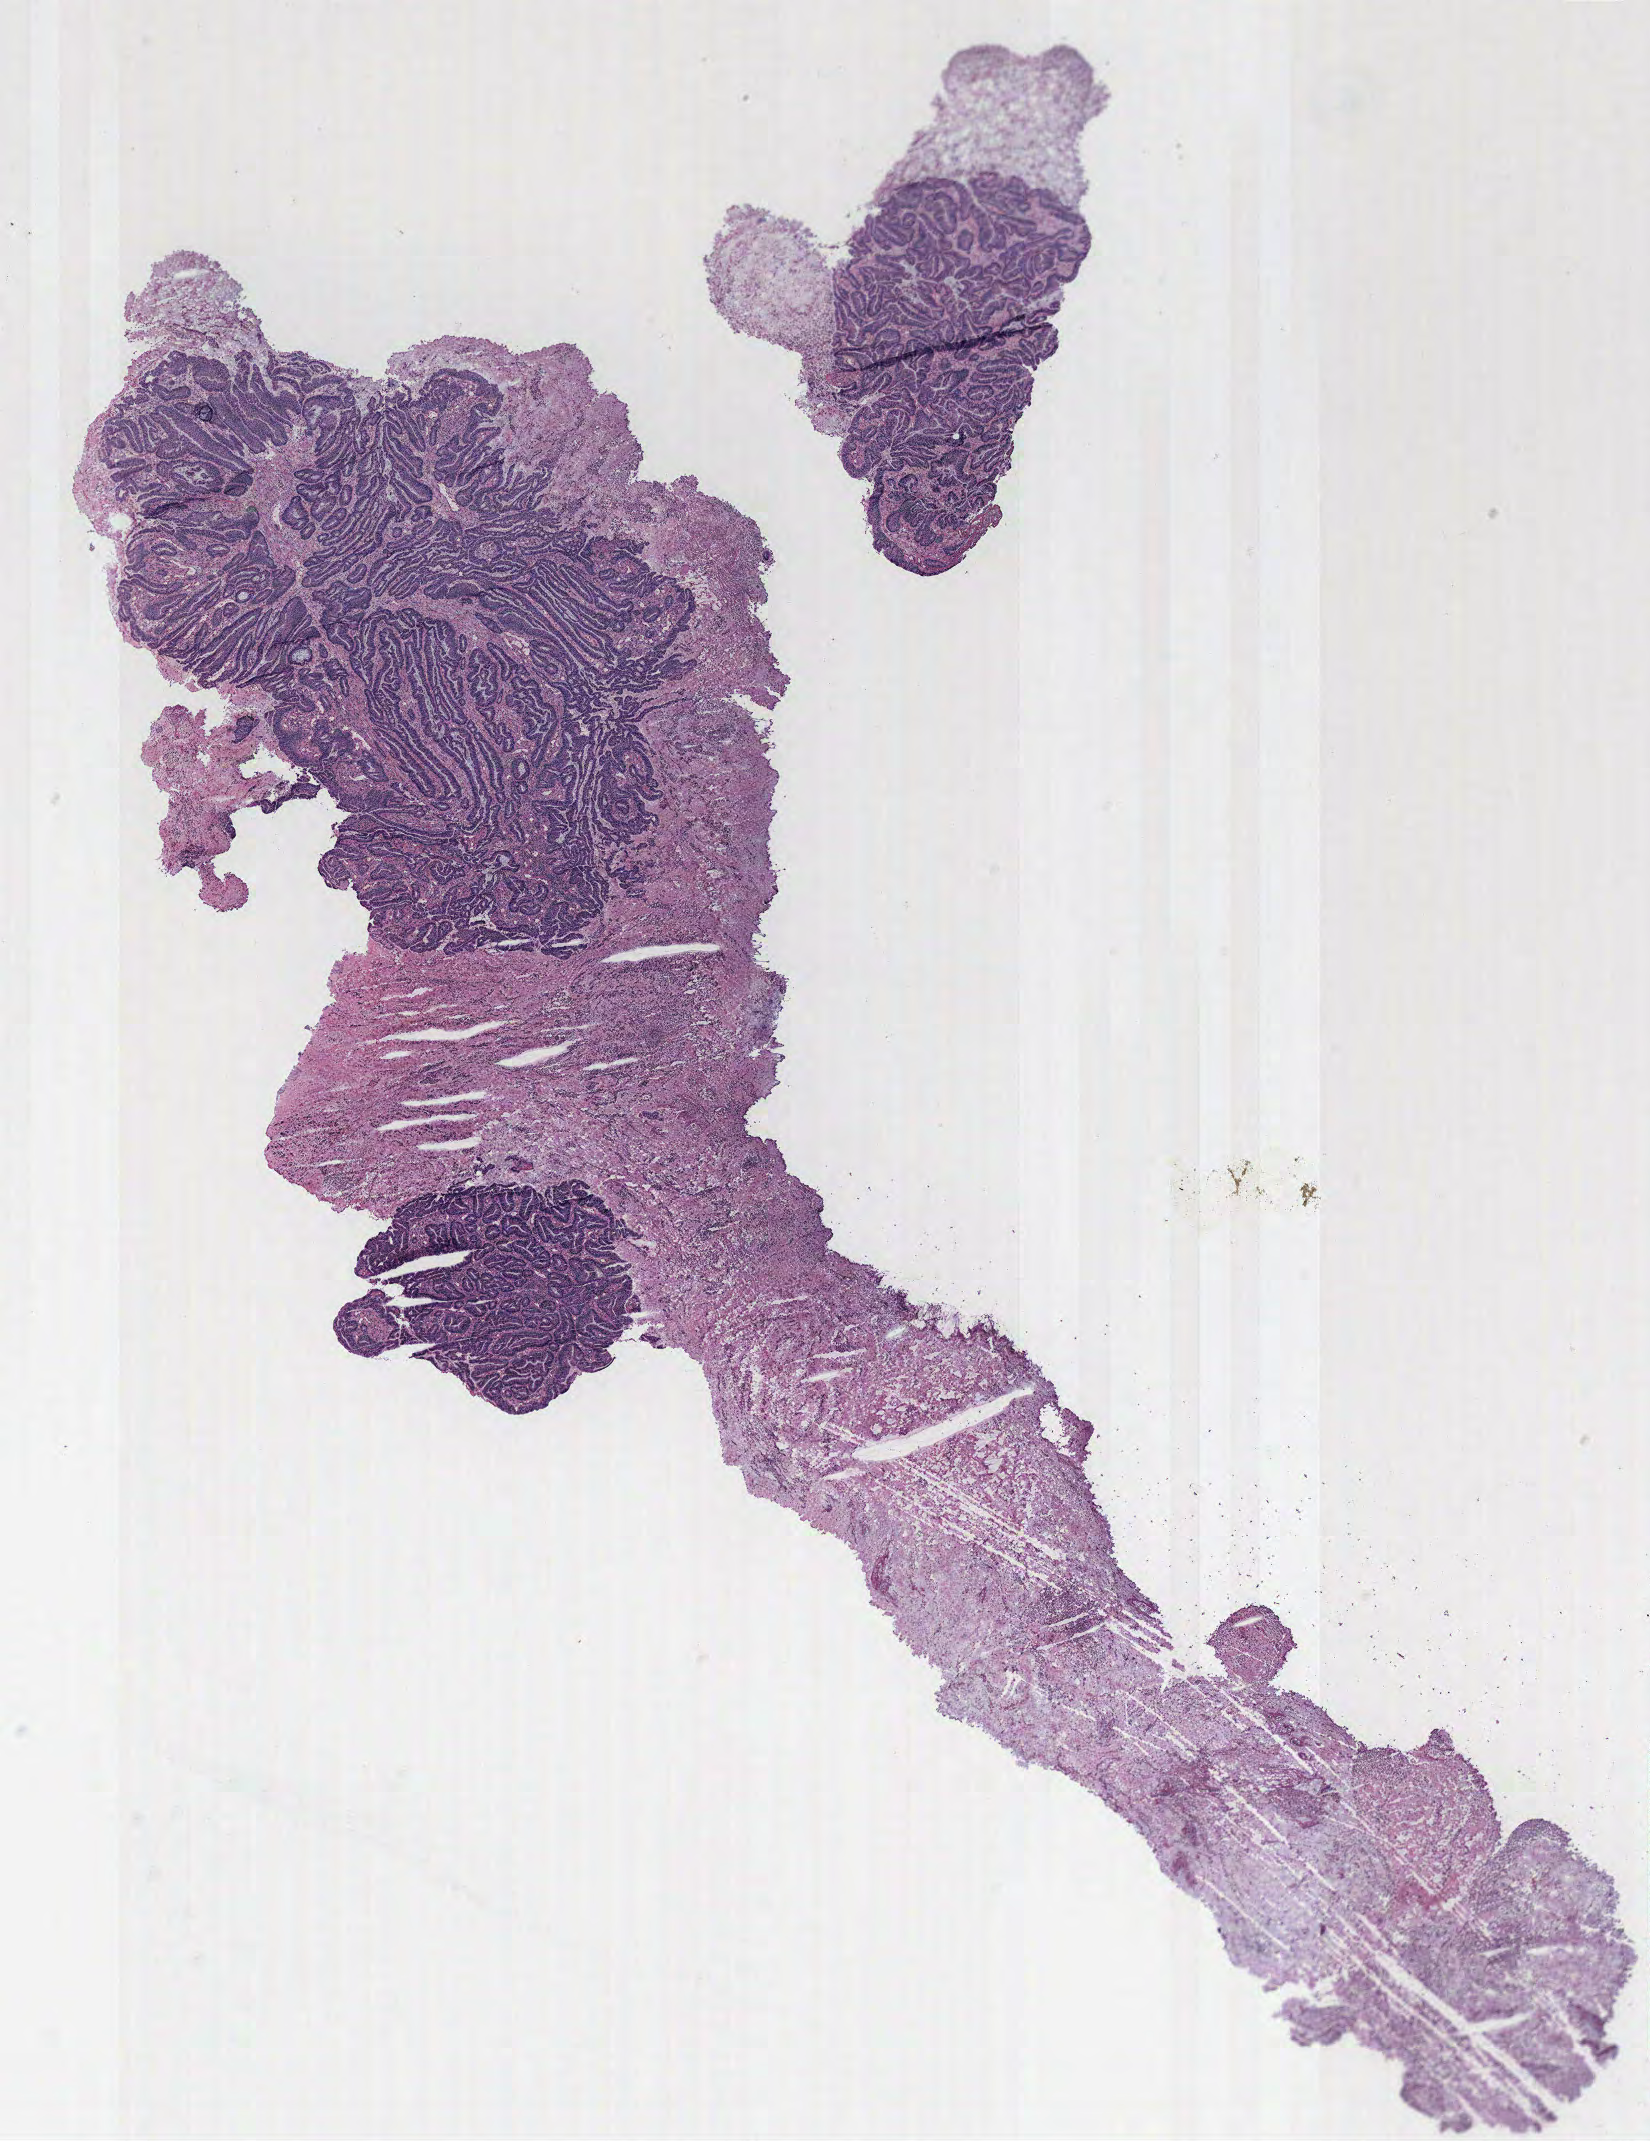
H&E whole-slide image — low-resolution overview of the scanned area, about 13.2 x 17.1 mm (from a 40x scan); colon, normal (non-tumour) tissue. Patient: female, age 76 years.
- this section: normal (non-tumour) tissue from the same patient
- patient diagnosis: Adenocarcinoma, NOS